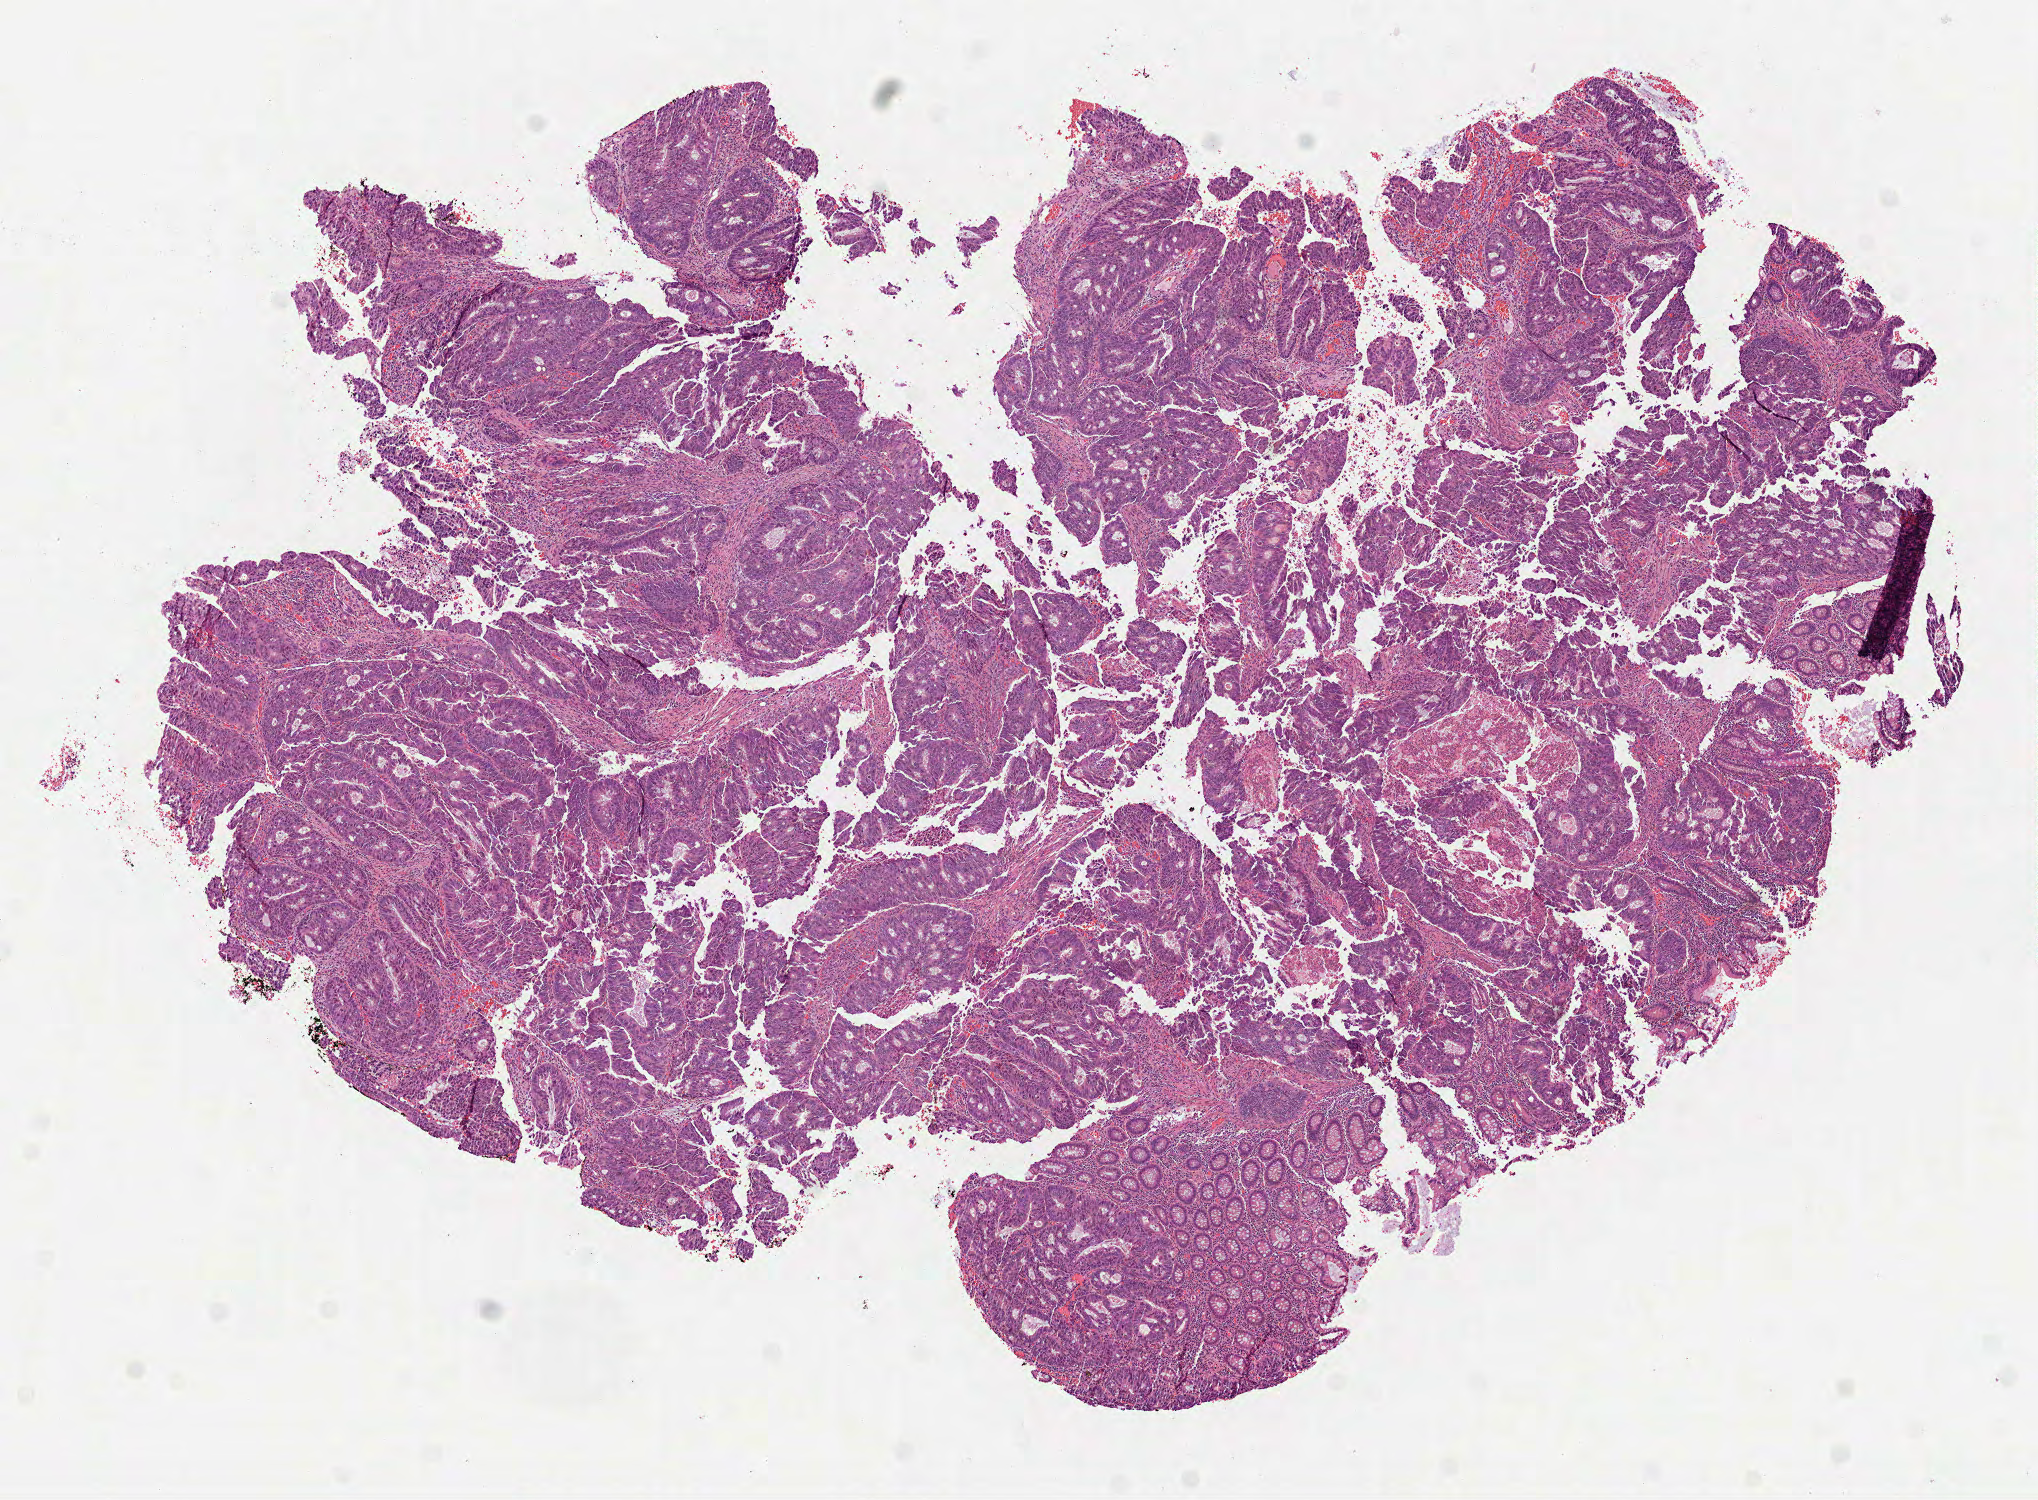
H&E-stained whole-slide image, a low-resolution overview of the entire scanned area, about 8.2 x 6.0 mm (from a 40x scan), formalin-fixed paraffin-embedded (FFPE) diagnostic section, primary tumour sample from the colon. Male patient; age at initial diagnosis 62 years.
- lymph nodes positive (case pathology): 11 of 17 examined
- AJCC pathologic stage: IIIC (7th edition)
- pathologic diagnosis: Adenocarcinoma, NOS
- TNM: T4a N2b M0